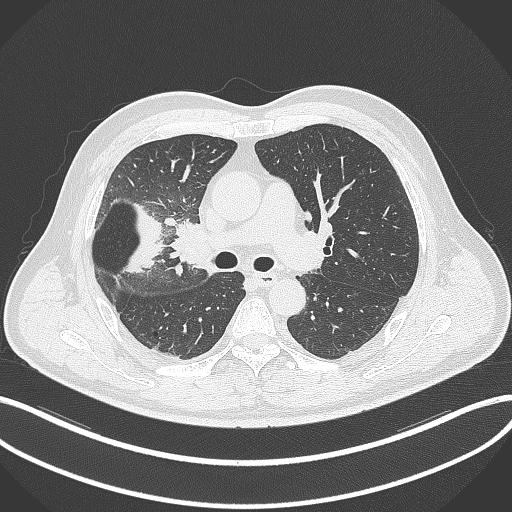
Chest CT, one axial slice; slice 202 of 348 in the series (ordered by position); reconstruction kernel B70f; 120 kVp; lung window (W 1500 / L -600 HU); 512 × 512 image matrix. Male patient, age 55 years. From the clinical record (not read from this slice): clinical TNM (as recorded): T3 N2 M1.
Structures marked on this image (bounding box drawn by a radiologist):
- lung tumour (recorded histology: adenocarcinoma): bounding box <120,200,169,280> (left, top, right, bottom; pixels)